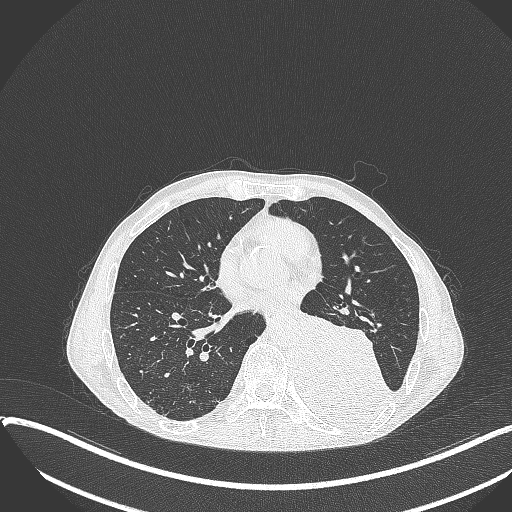
Chest CT, one axial slice; position 157 of 401 along the scan axis; 120 kVp; lung window (W 1500 / L -600 HU); 1 mm slice thickness; 512 × 512 image matrix, field of view 400 × 400 mm. Patient: male, 57 years. From the clinical record (not read from this slice): clinical TNM (as recorded): T4 N0 M0.
Annotated regions visible in this slice (bounding box drawn by a radiologist):
- lung tumour (recorded histology: squamous cell carcinoma): bounding box [x1, y1, x2, y2] px = [296, 311, 396, 425]